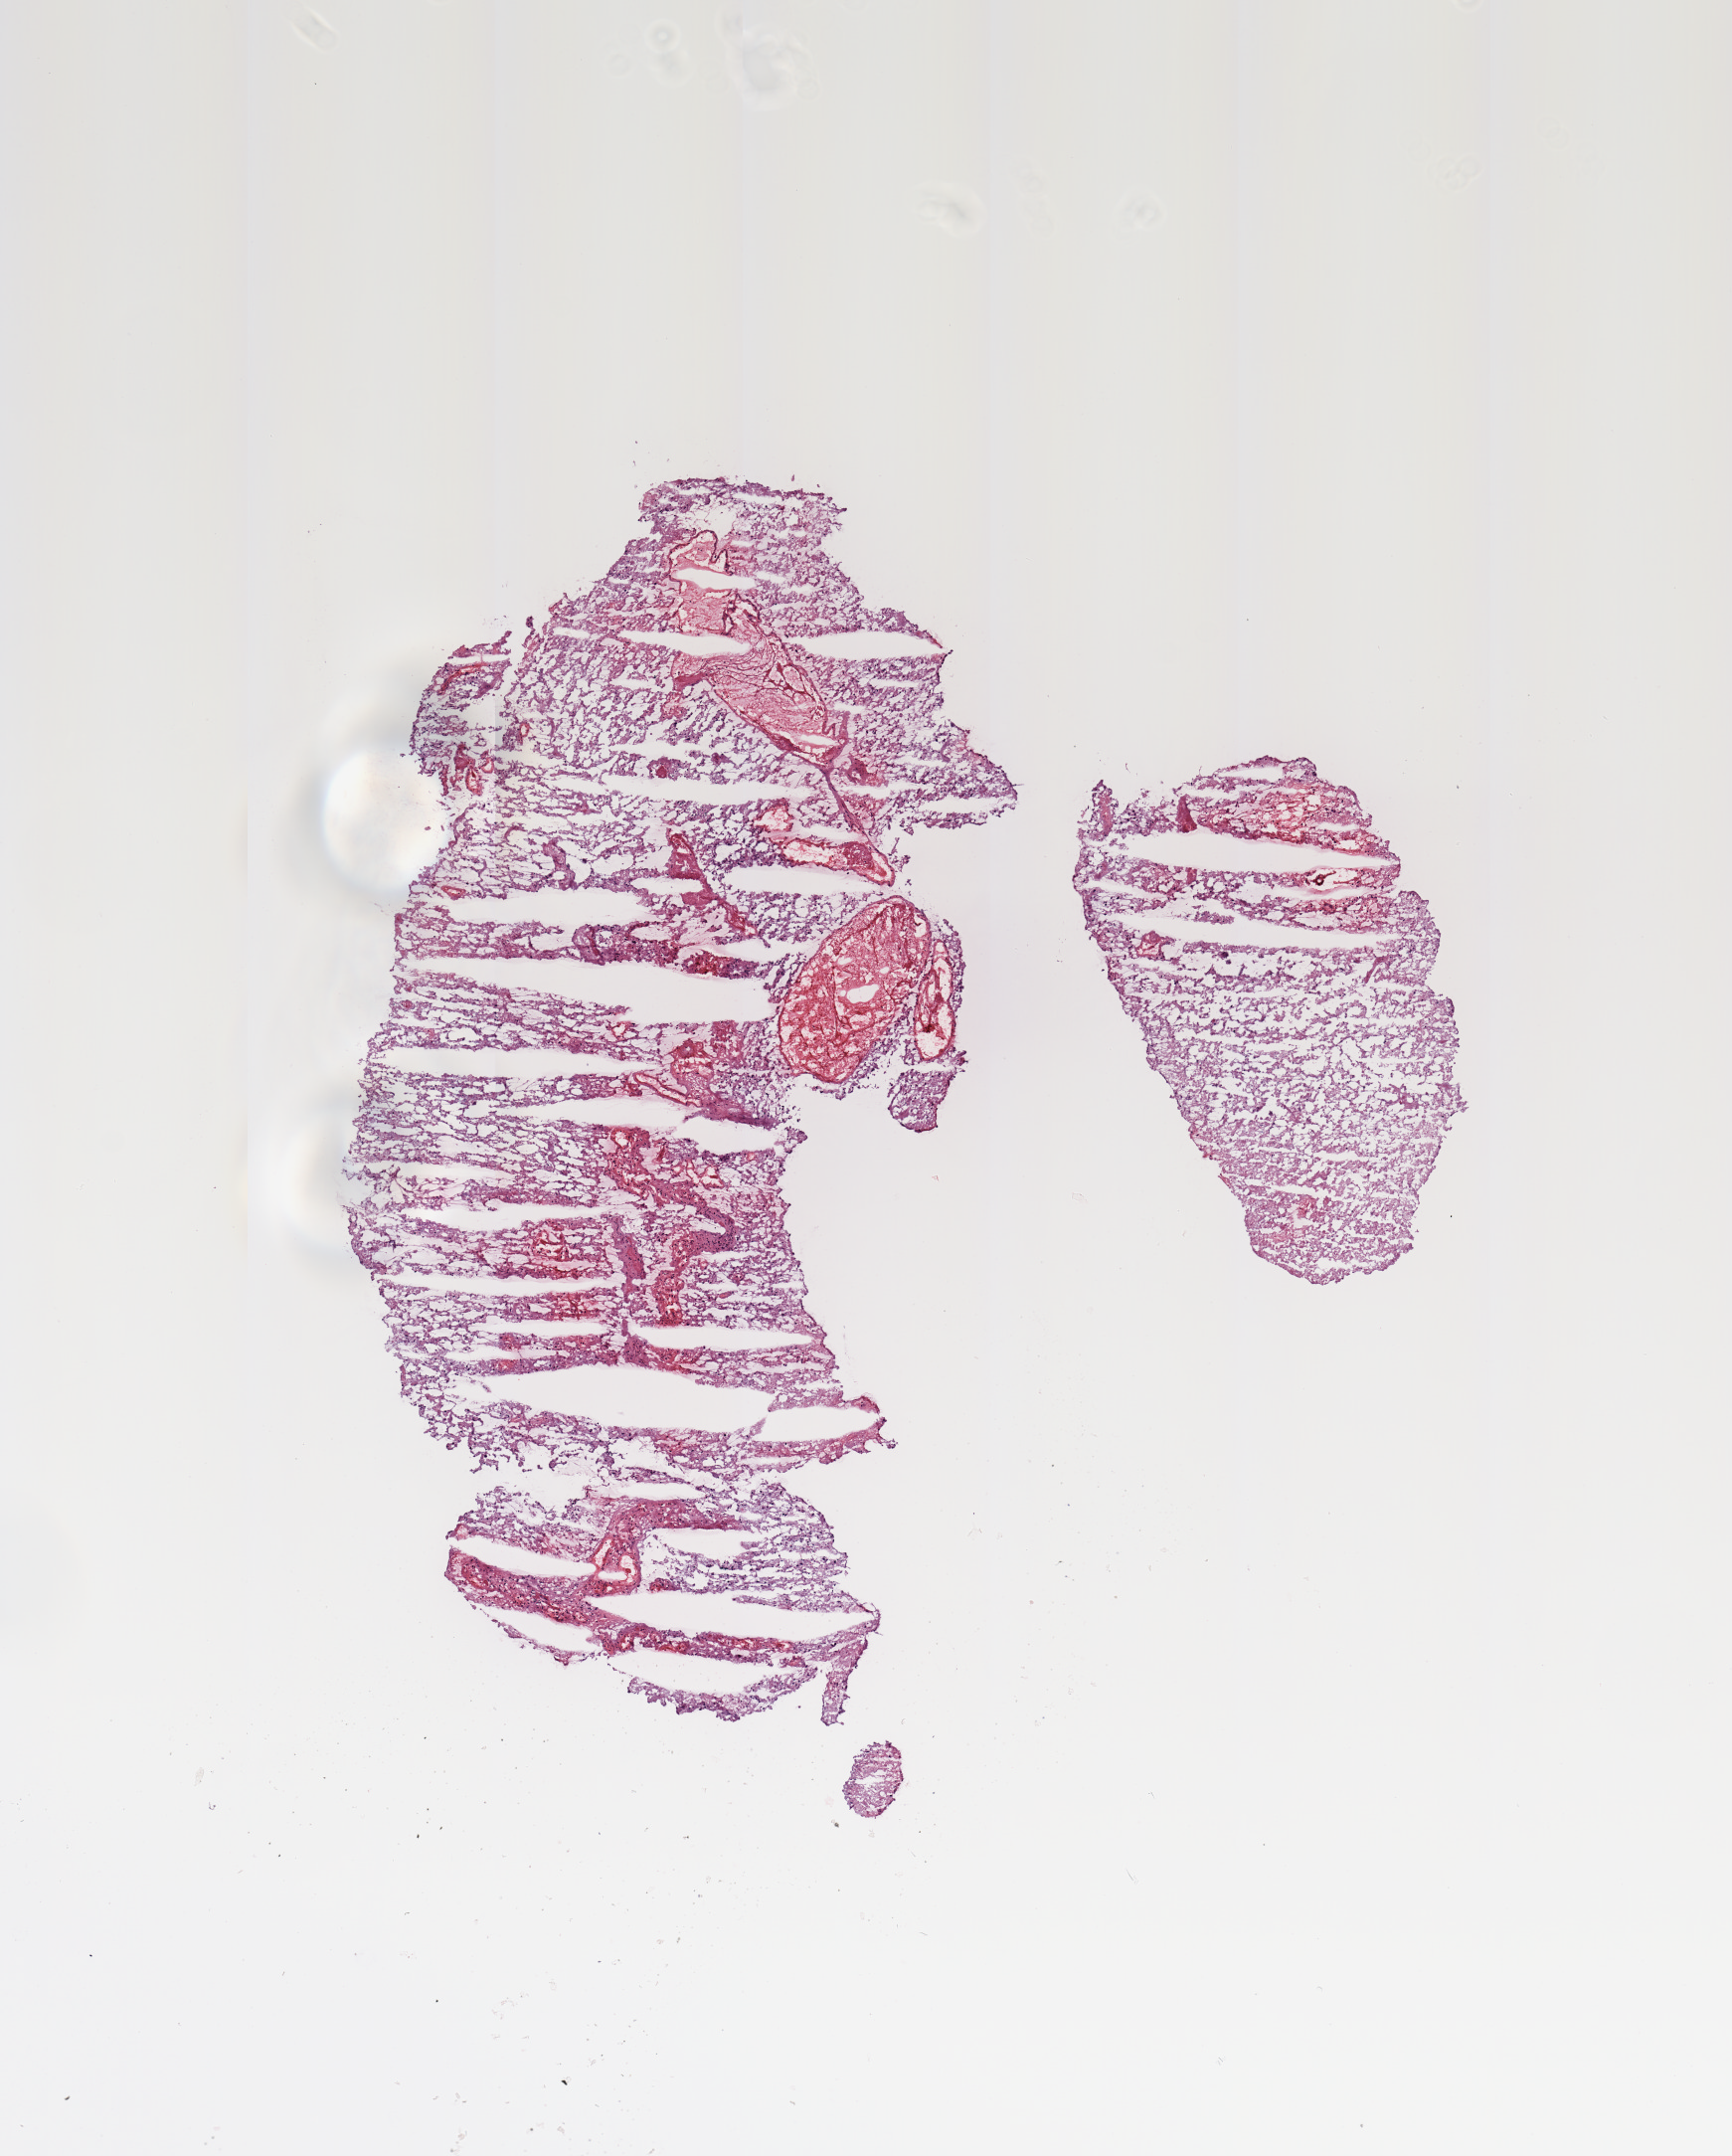
H&E-stained whole-slide image — shown as a low-resolution overview of the whole scanned area (about 6.9 x 8.6 mm, from a 20x scan); tumour tissue sample, brain. Female, 57 y/o.
Patient diagnosis (cohort enrolment): glioblastoma multiforme (brain). Primary tumour site (as recorded): temporal lobe.